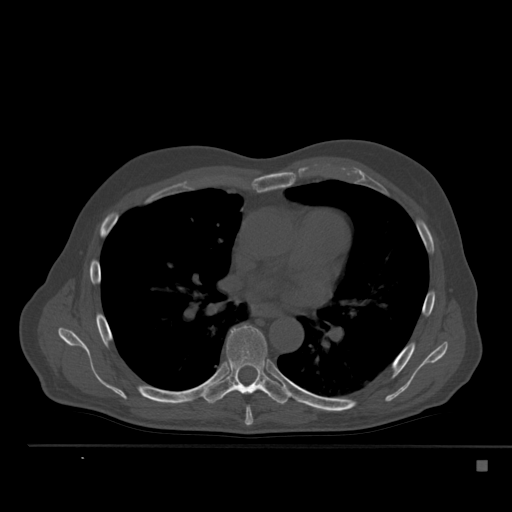
CT including the spine, one axial slice; position 333 of 517 along the scan axis; 120 kVp; bone window (W 1800 / L 400 HU); 512 × 512 image matrix, field of view 408 × 408 mm. Patient: male, 70 years. Case-level facts recorded for this patient, not image findings: primary cancer: renal.
Annotated regions visible in this slice (semi-automatically segmented with operator editing):
- T6 vertebra: bounding box [x1, y1, x2, y2] px = [245, 407, 253, 426]
- T7 vertebra: [202, 325, 291, 405]